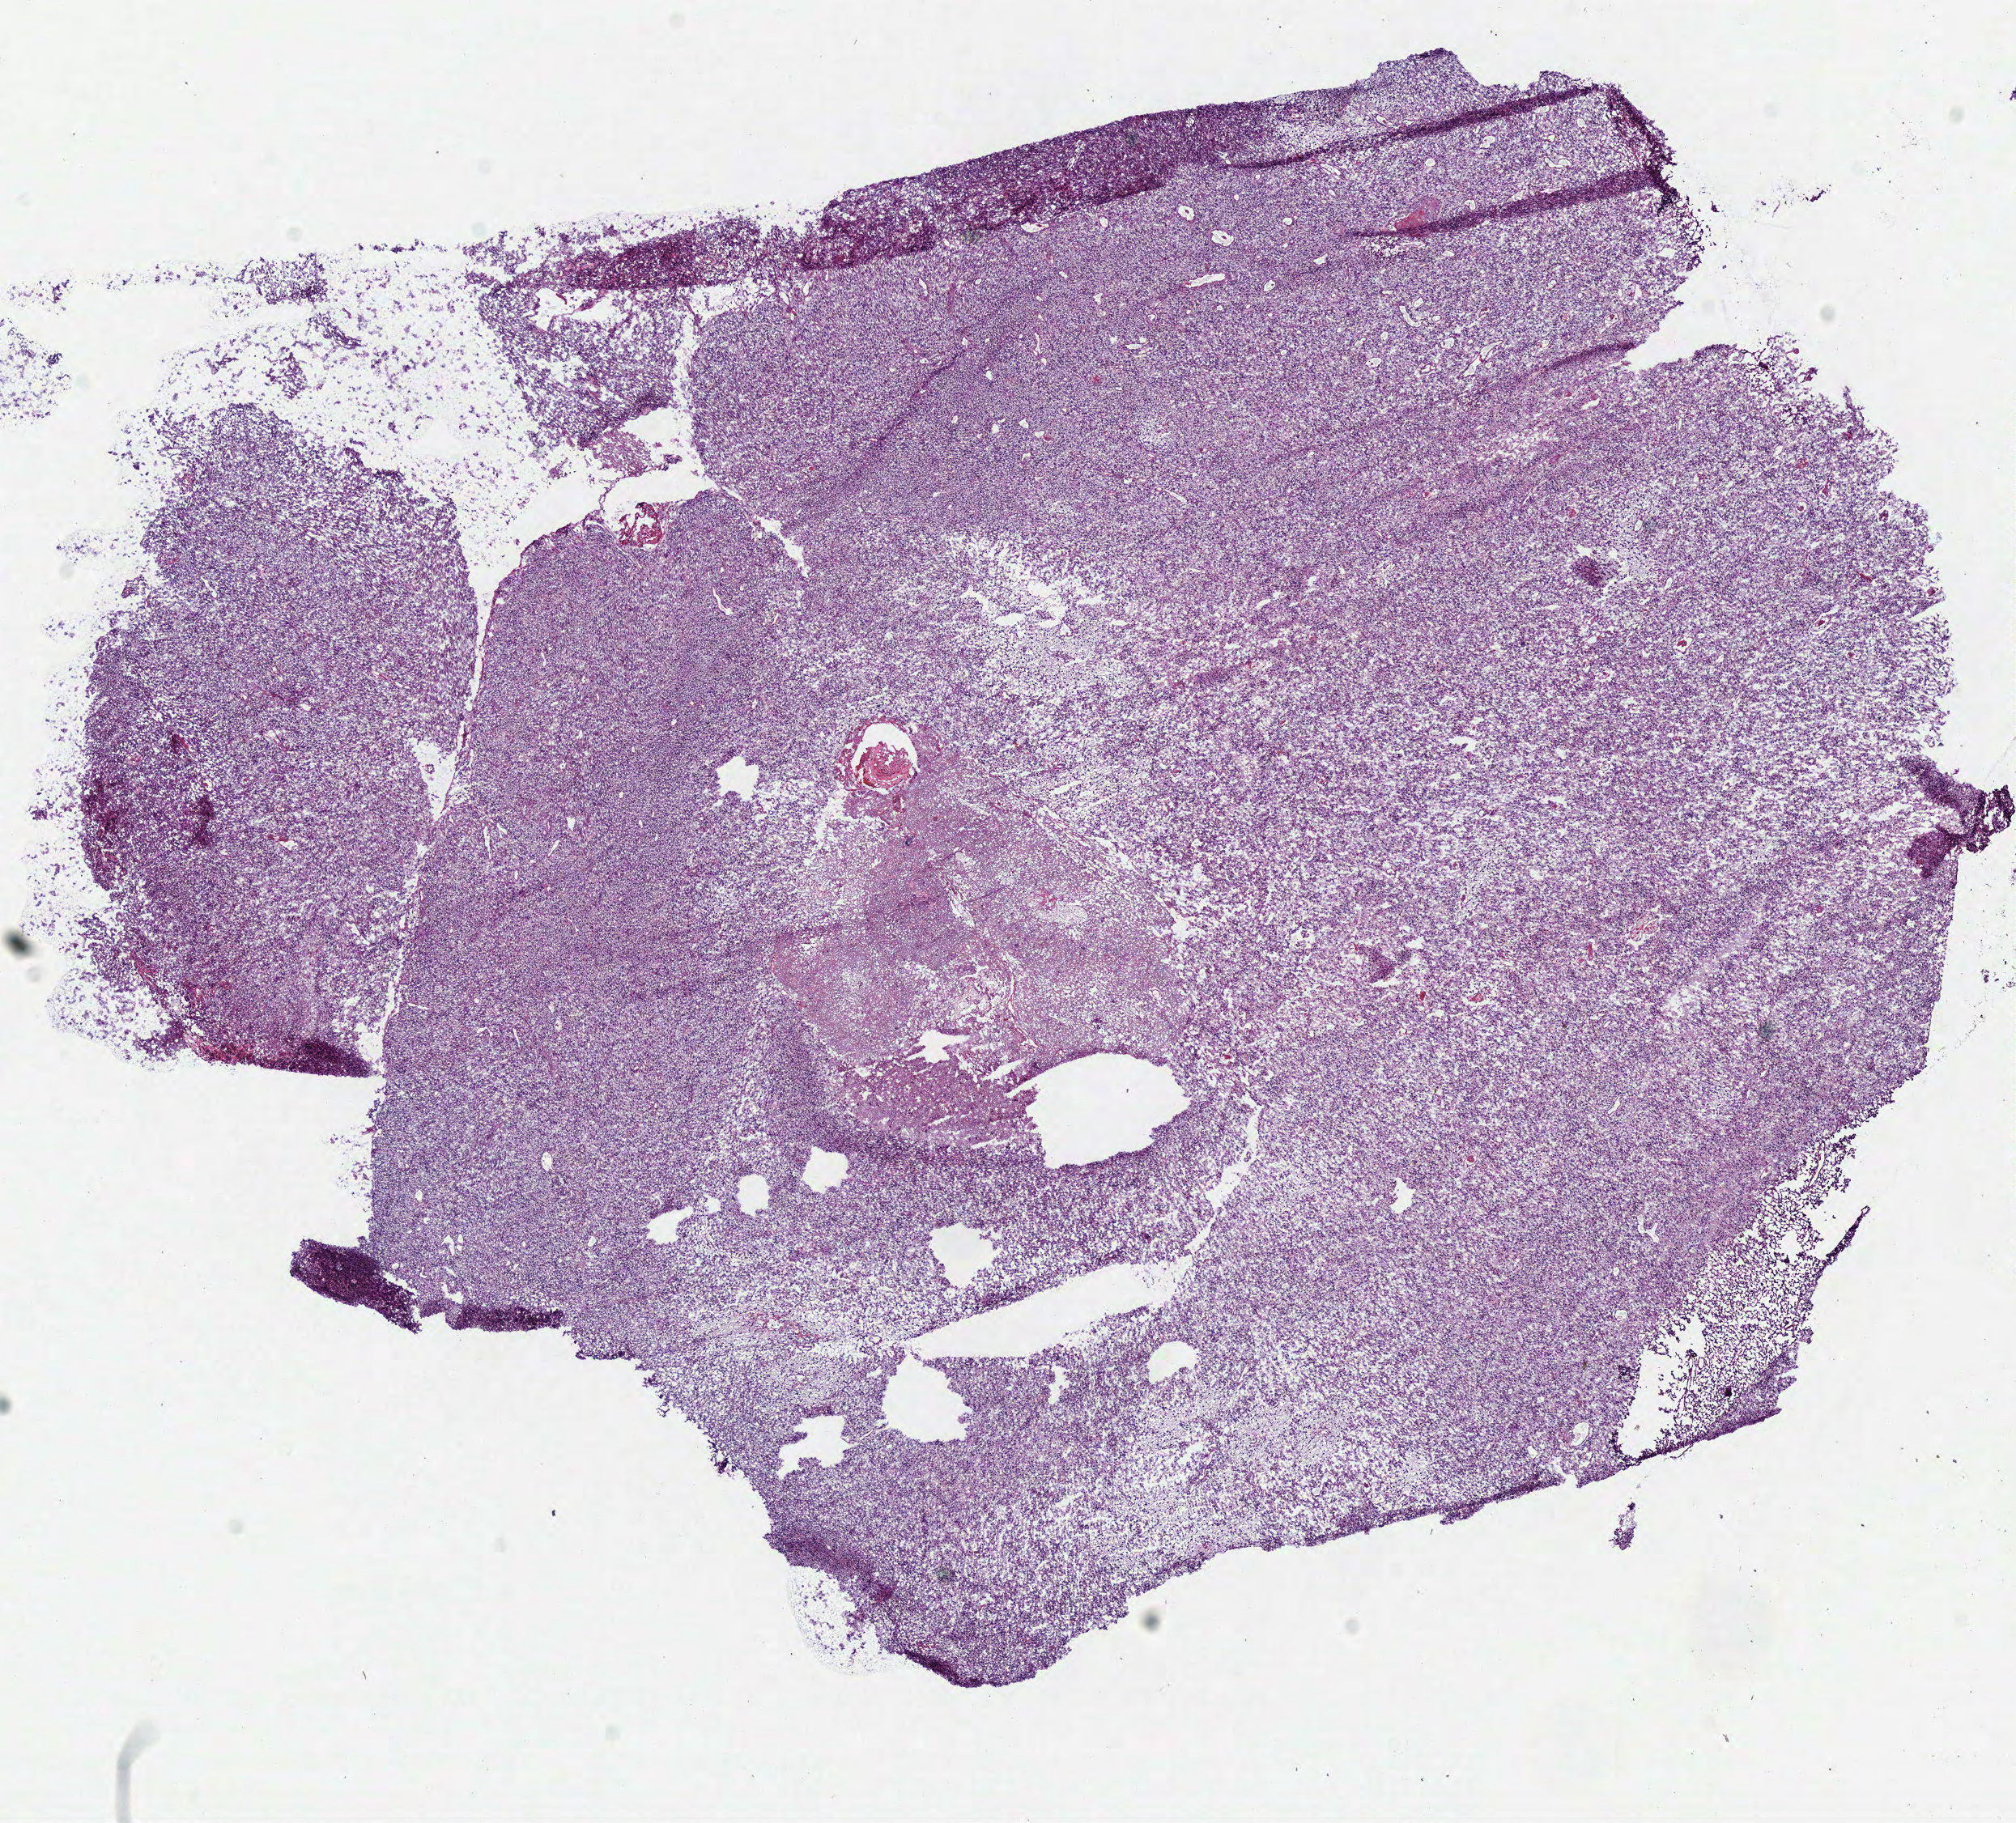
Digitized H&E tissue section (whole slide), shown as a low-resolution overview of the whole scanned area (about 9.8 x 8.9 mm, slide scanned at 40x). Frozen section from the bottom of the tissue portion. Sample: primary tumour, brain. Female patient; age at initial diagnosis 64 years. Pathologist review of this section (percent, as recorded): tumour cells 94%, tumour nuclei 80%, normal cells 5%, stromal cells 0%, necrosis 1%.
- diagnosis: Glioblastoma